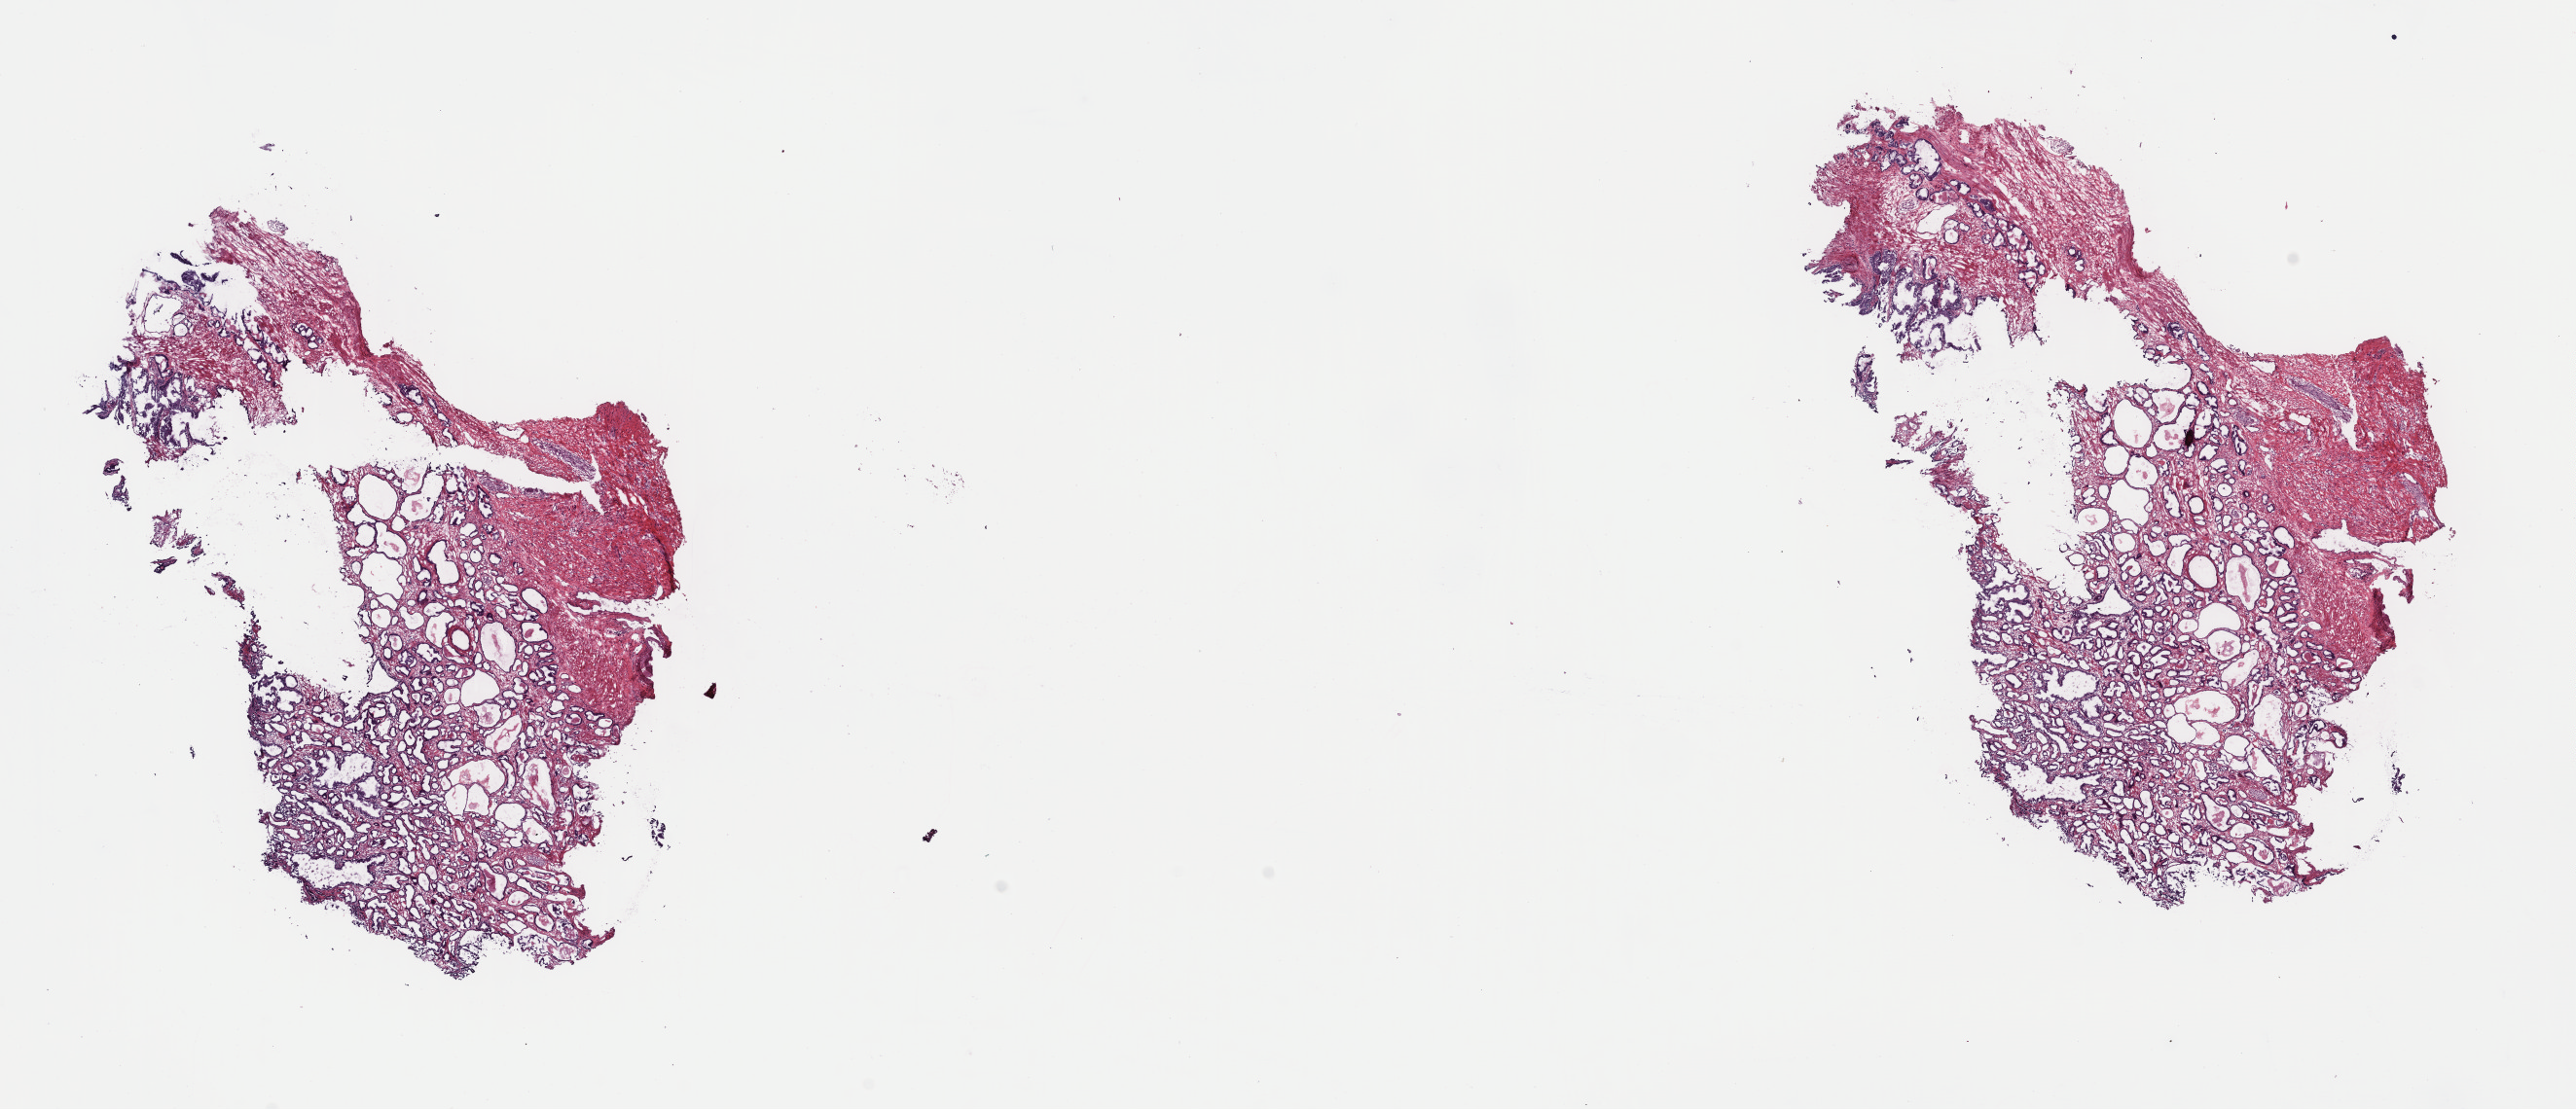
H&E whole-slide image, low-resolution overview of the scanned area, about 20.9 x 9.0 mm (acquisition: 40x scan), frozen section, prostate, primary tumour sample. Male, age 55 years at initial diagnosis. Gleason score: 7 (3+4). Slide review estimates, as recorded: tumour cells 75%, tumour nuclei 70%, normal cells 25%, stromal cells 0%, necrosis 0%. Infiltration values recorded for this section: lymphocyte infiltration 2%, monocyte infiltration 0%, neutrophil infiltration 0%.
Diagnosis: Adenocarcinoma, NOS (prostate gland). Laterality: right.